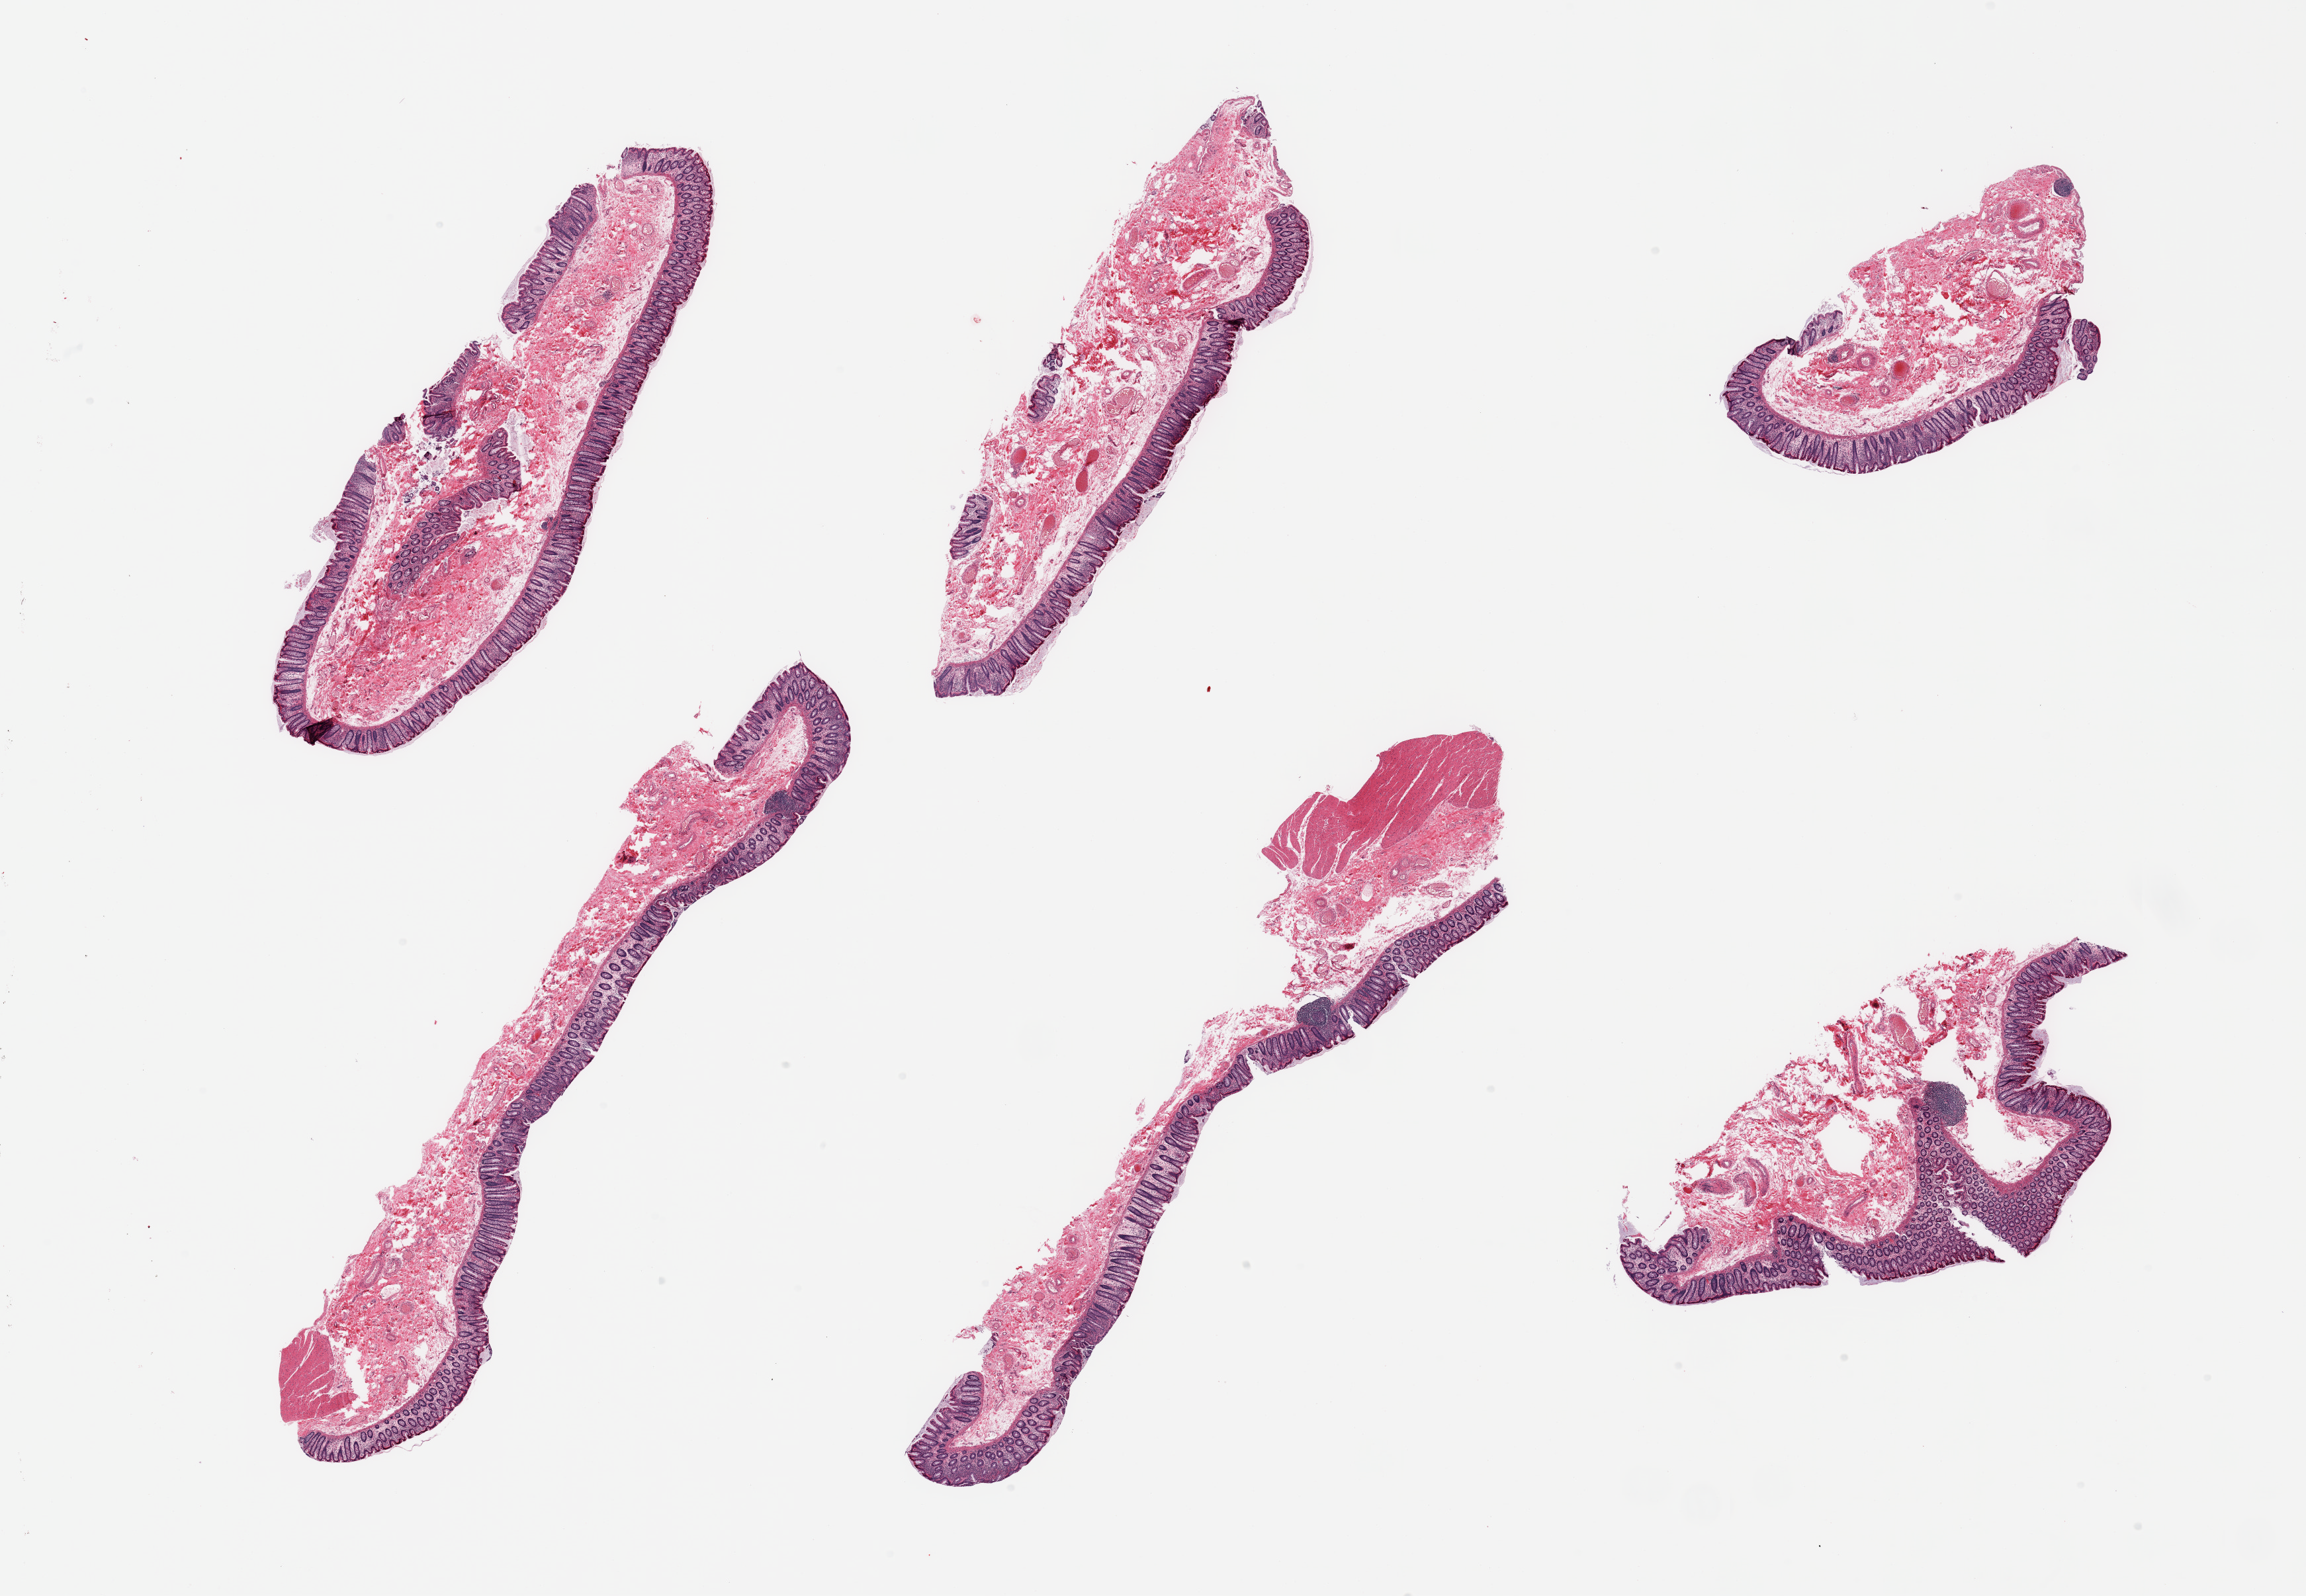
H&E whole-slide image — a low-resolution overview of the entire scanned area, about 27.6 x 19.1 mm; PAXgene-fixed paraffin-embedded (PFPE) section; section of transverse colon (target tissue); donor tissue sample. Female donor.
Review note (as recorded): 6 pieces; predominantly mucosa and submucosa only with small portion of muscularis in 2 pieces.